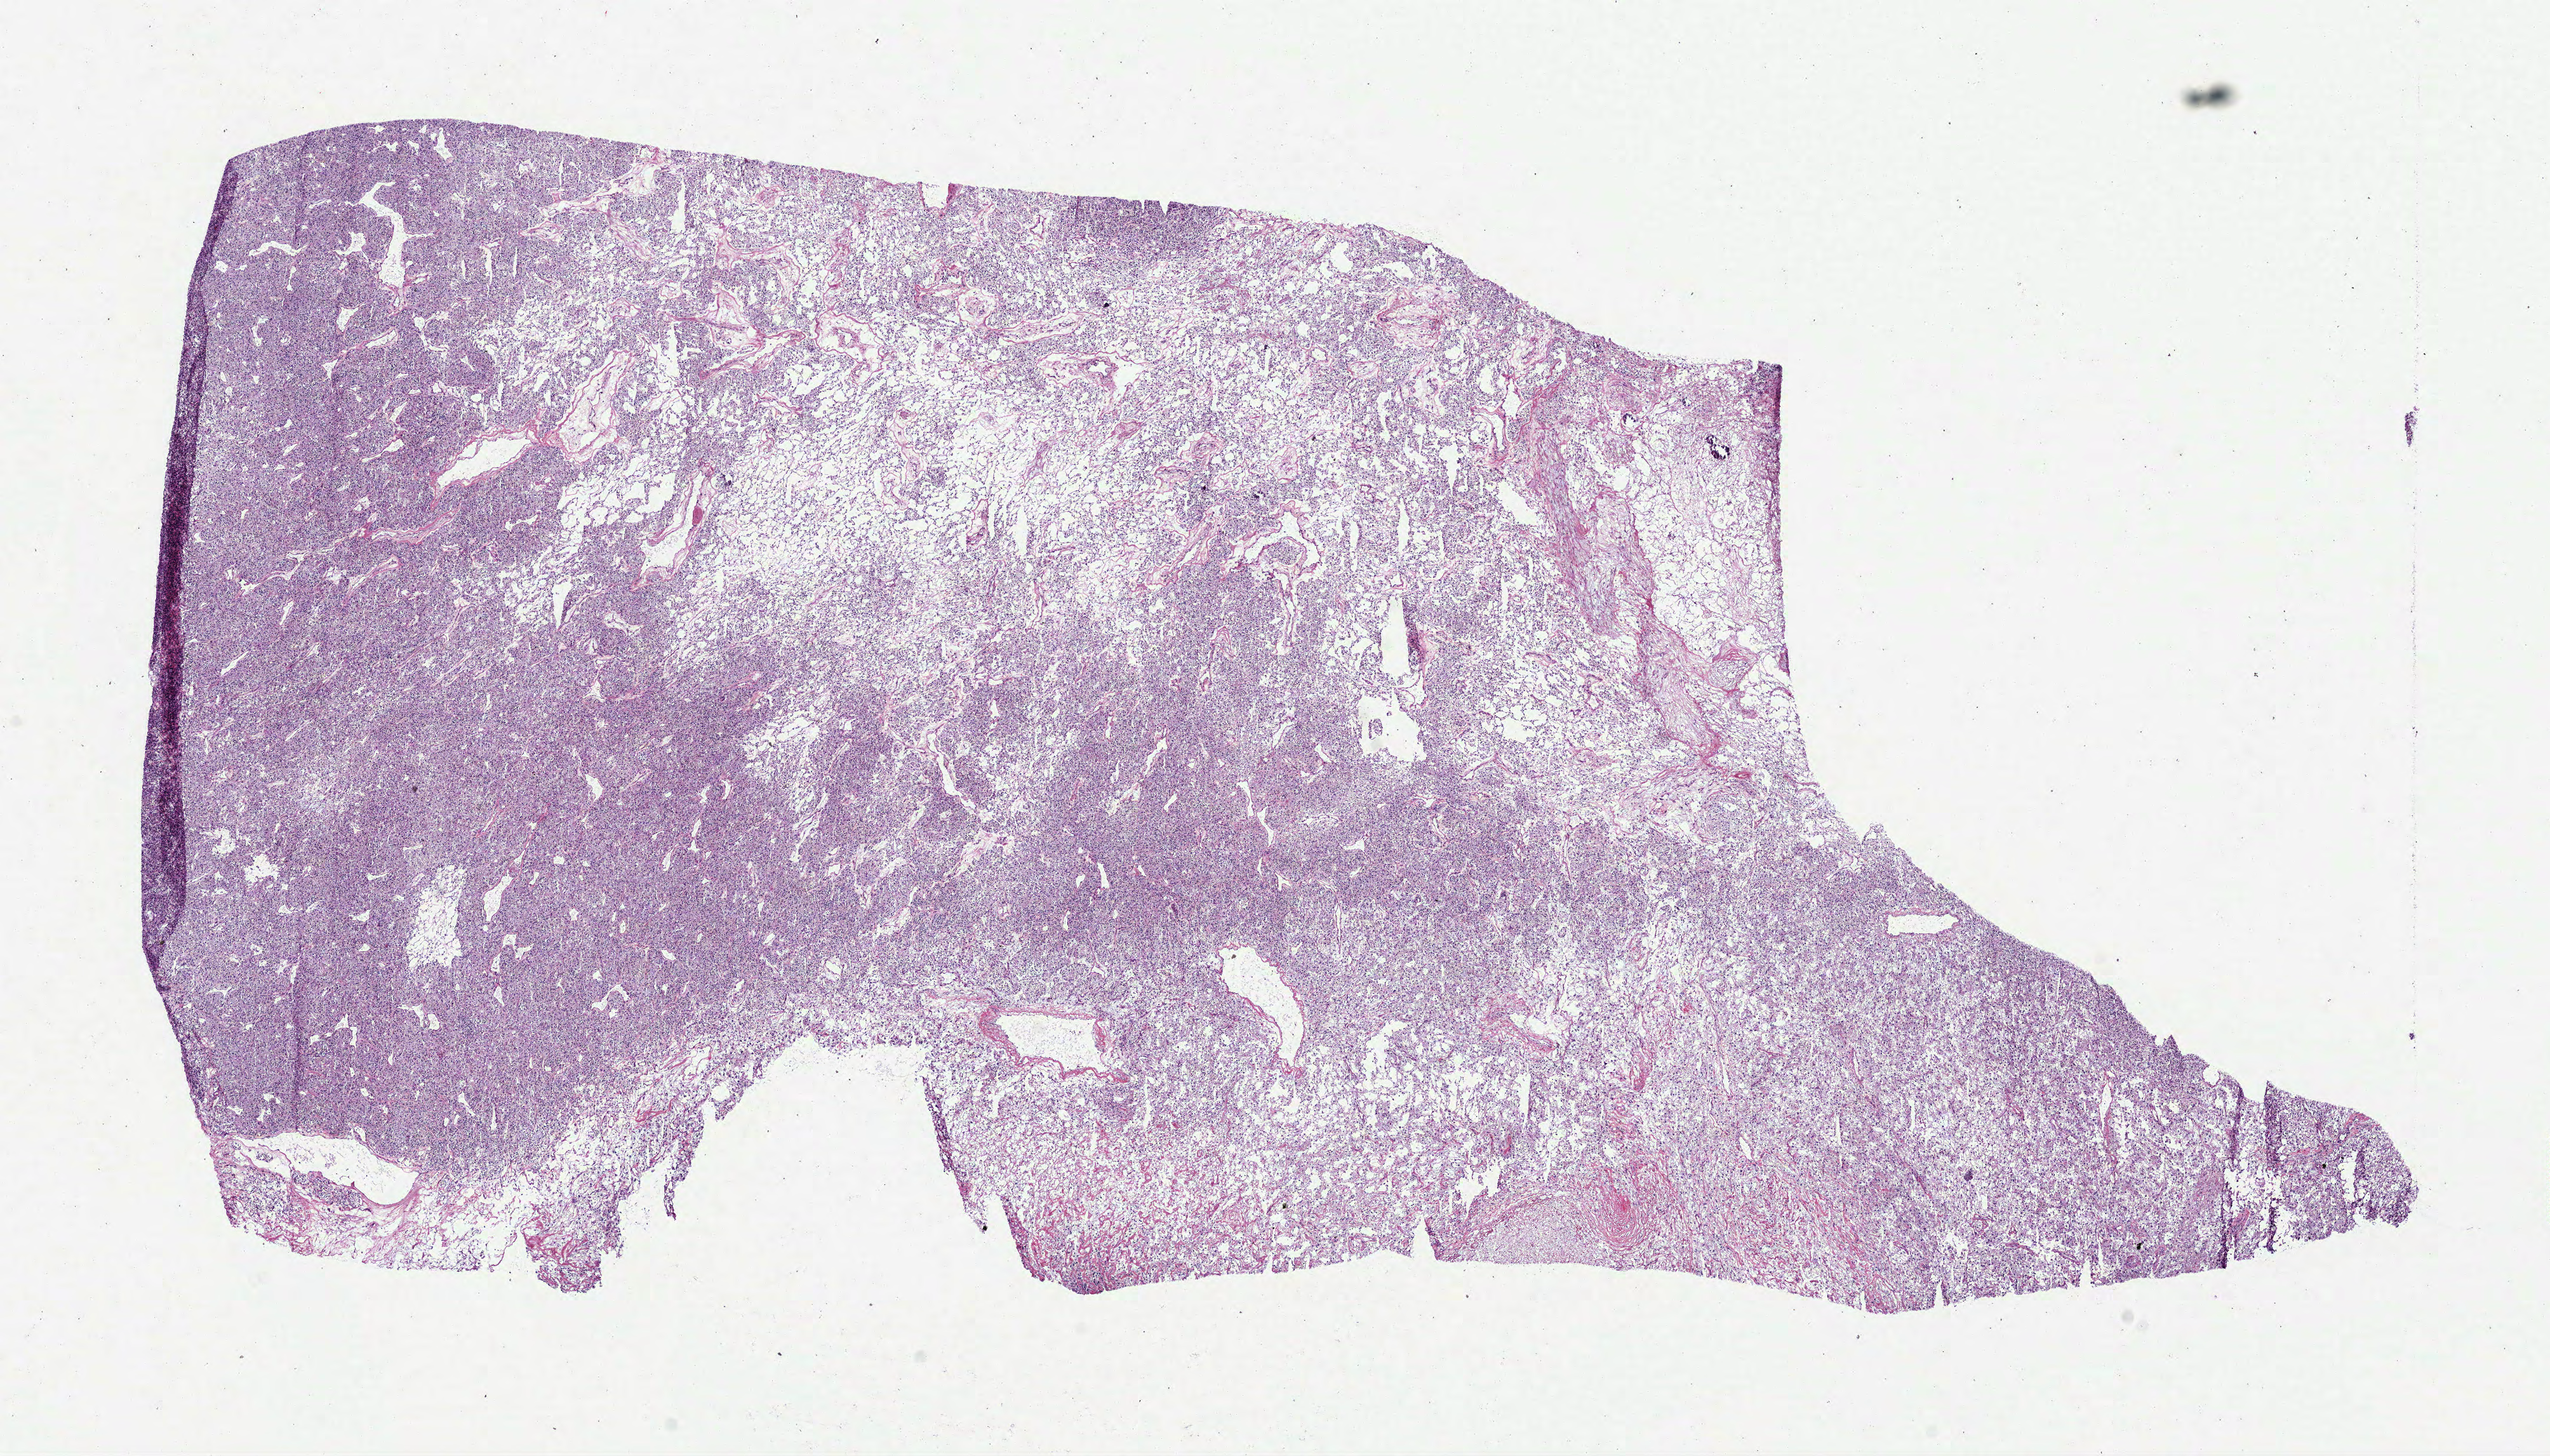
Hematoxylin and eosin (H&E) stained whole-slide image — whole scanned area (about 16.2 x 9.2 mm, from a 40x scan) shown as a low-resolution overview; frozen section from the bottom of the tissue portion; primary tumour sample from the kidney. Patient: male, age at initial diagnosis 81 years.
Diagnosis: Clear cell adenocarcinoma, NOS.